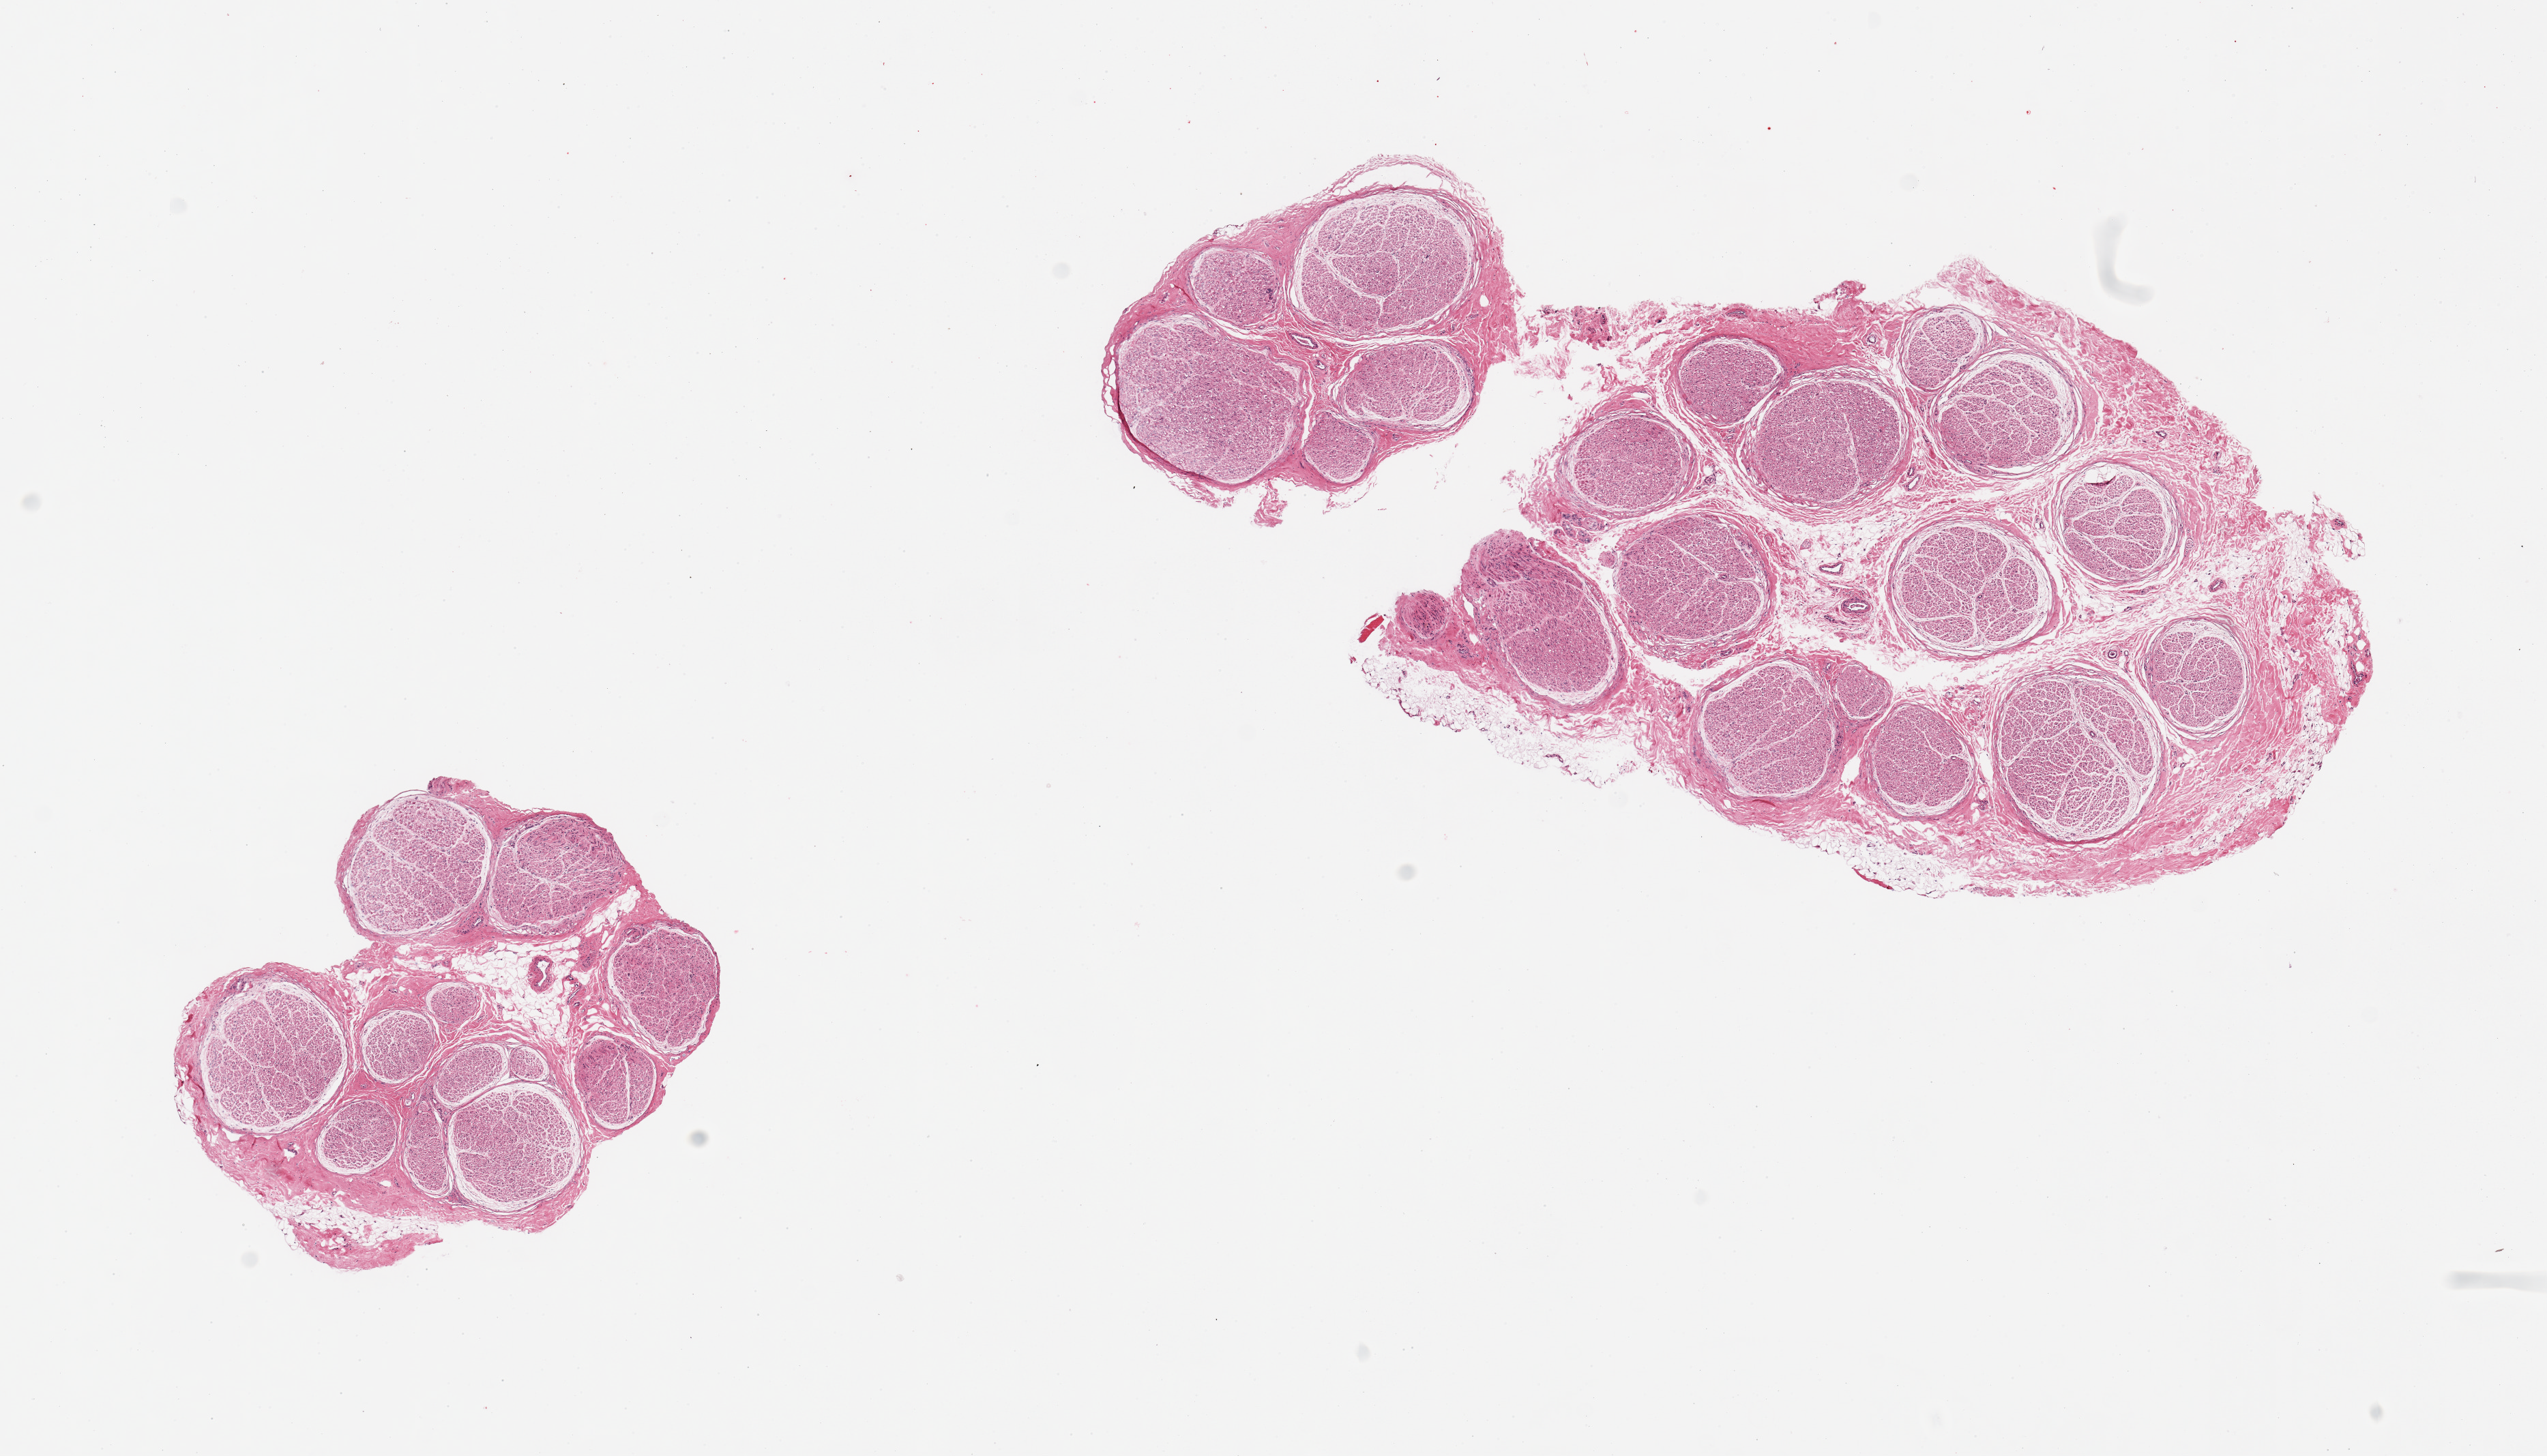
Hematoxylin and eosin (H&E) whole-slide image, brightfield — shown as a low-resolution overview of the whole scanned area (about 14.8 x 8.4 mm, acquisition: 20x scan). PAXgene-fixed, paraffin-embedded tissue. Sampled site (target tissue): tibial nerve. Donor tissue sample. Donor sex: female.
Pathologist's review note for this sample: 2 pieces; 5% fat.